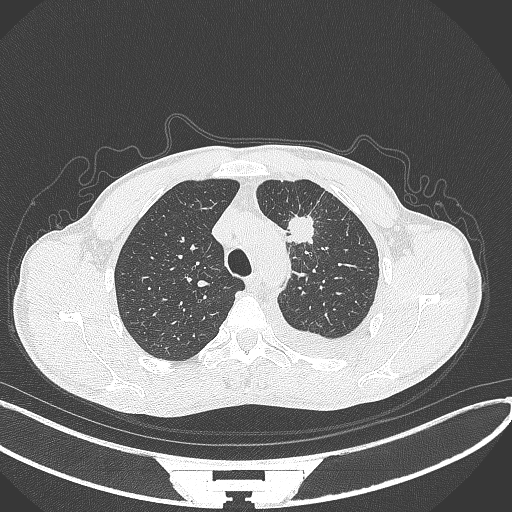
Chest CT, one axial slice; slice 262 of 371 in the series (ordered by position); reconstruction kernel B70f; 120 kVp; lung window (W 1500 / L -600 HU); 512 × 512 image matrix, field of view 400 × 400 mm. Male patient, age 49 years. Case-level facts recorded for this patient, not image findings: clinical TNM (as recorded): T1c N1 M1.
Annotated regions visible in this slice (bounding box drawn by a radiologist):
- lung tumour (recorded histology: adenocarcinoma): box from (x=282, y=209) to (x=322, y=253) px